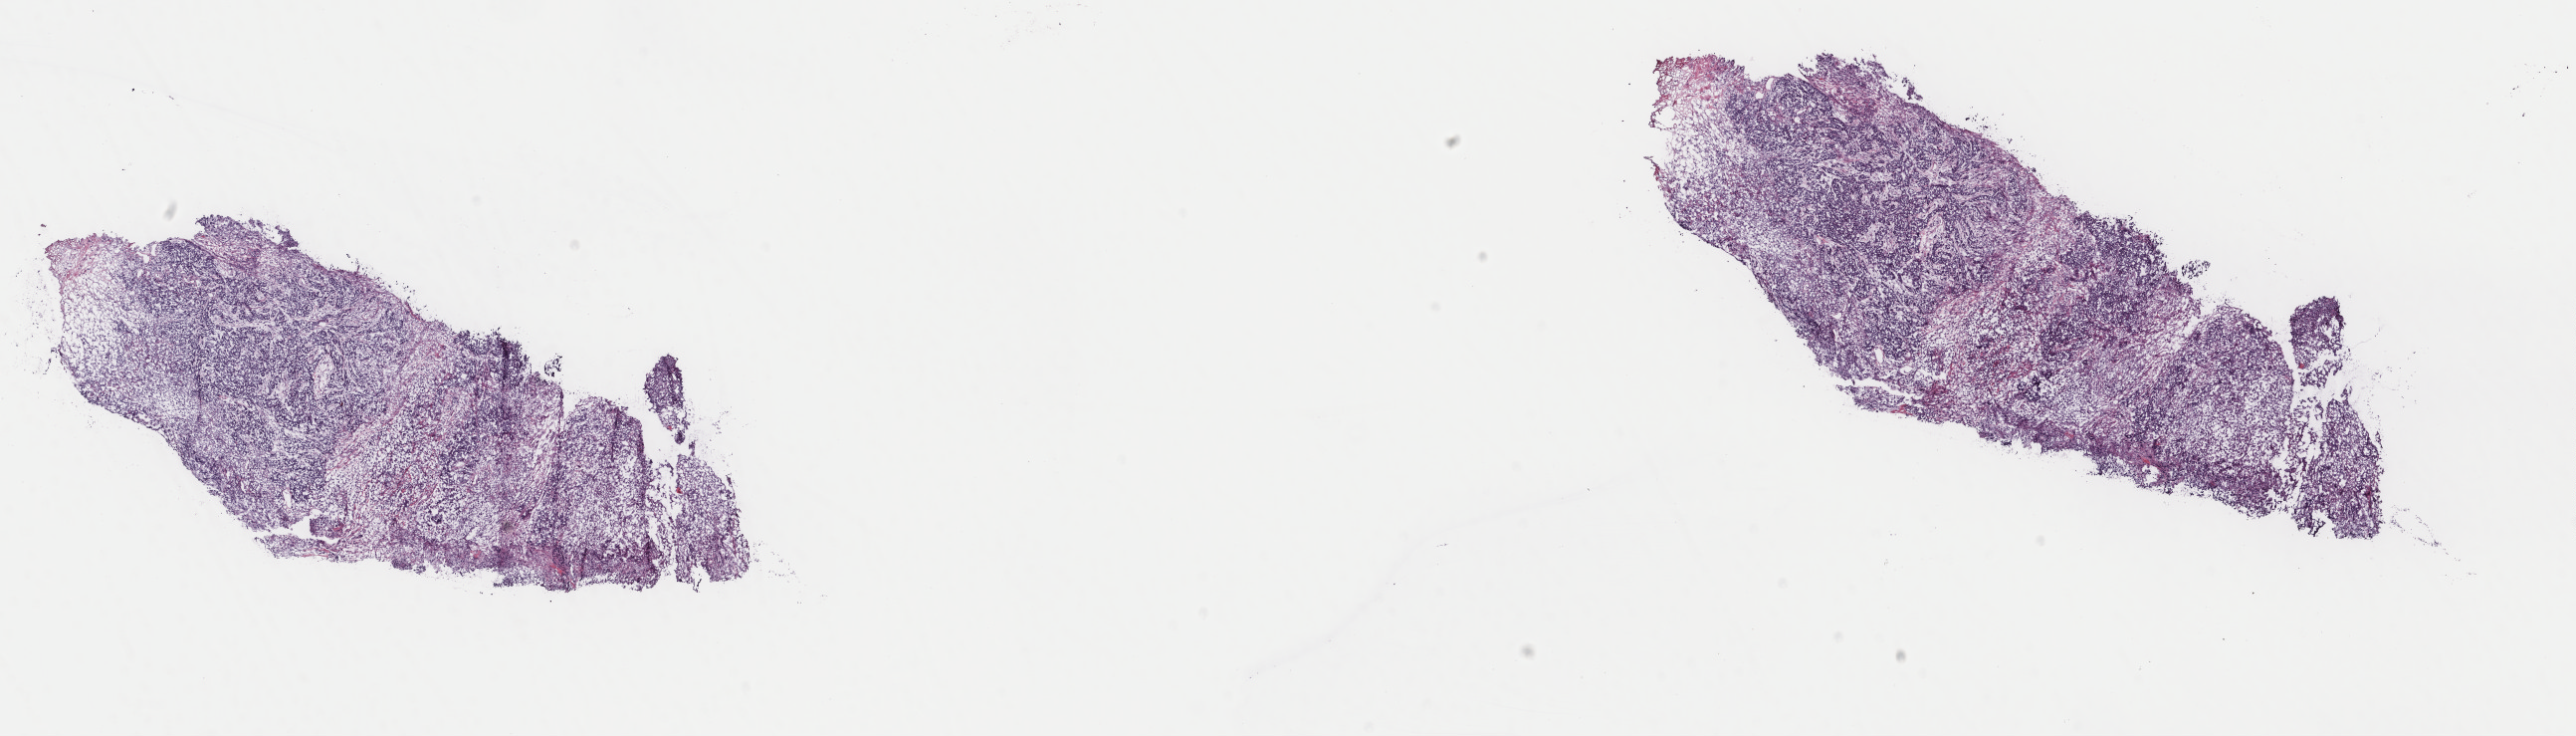
Whole-slide histology image, Hematoxylin and eosin (H&E) stained — whole scanned area (about 20.5 x 5.9 mm, from a 40x scan) shown as a low-resolution overview; frozen section; primary tumour sample from the uterus. Female, age 77 years at initial diagnosis. Slide review estimates, as recorded: tumour cells 90%, tumour nuclei 90%, normal cells 5%, stromal cells 5%, necrosis 0%. Inflammatory infiltration, as recorded: lymphocyte infiltration 60%, monocyte infiltration 10%, neutrophil infiltration 5%.
- diagnosis: Mullerian mixed tumor
- FIGO stage: IIIC2
- lymph nodes positive (case pathology): 1 of 3 examined